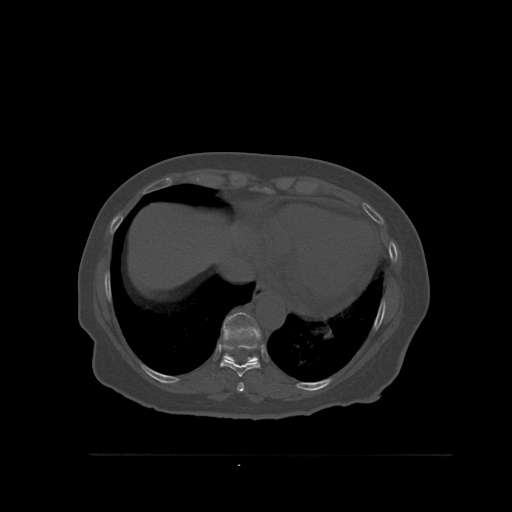
CT including the spine, one axial slice; position 331 of 527 along the scan axis; bone window (W 1800 / L 400 HU); 1.5 mm slice thickness; 512 × 512 image matrix. Patient: female, 73 years. Case-level facts recorded for this patient, not image findings: primary cancer: breast; vertebrae with lytic lesions (as recorded): L2.
Structures marked on this image (semi-automatically segmented with operator editing):
- T10 vertebra: bounding box (x1, y1, x2, y2) in pixels: (222, 312, 261, 363)
- T8 vertebra: (237, 382, 244, 392)
- T9 vertebra: (220, 336, 261, 377)